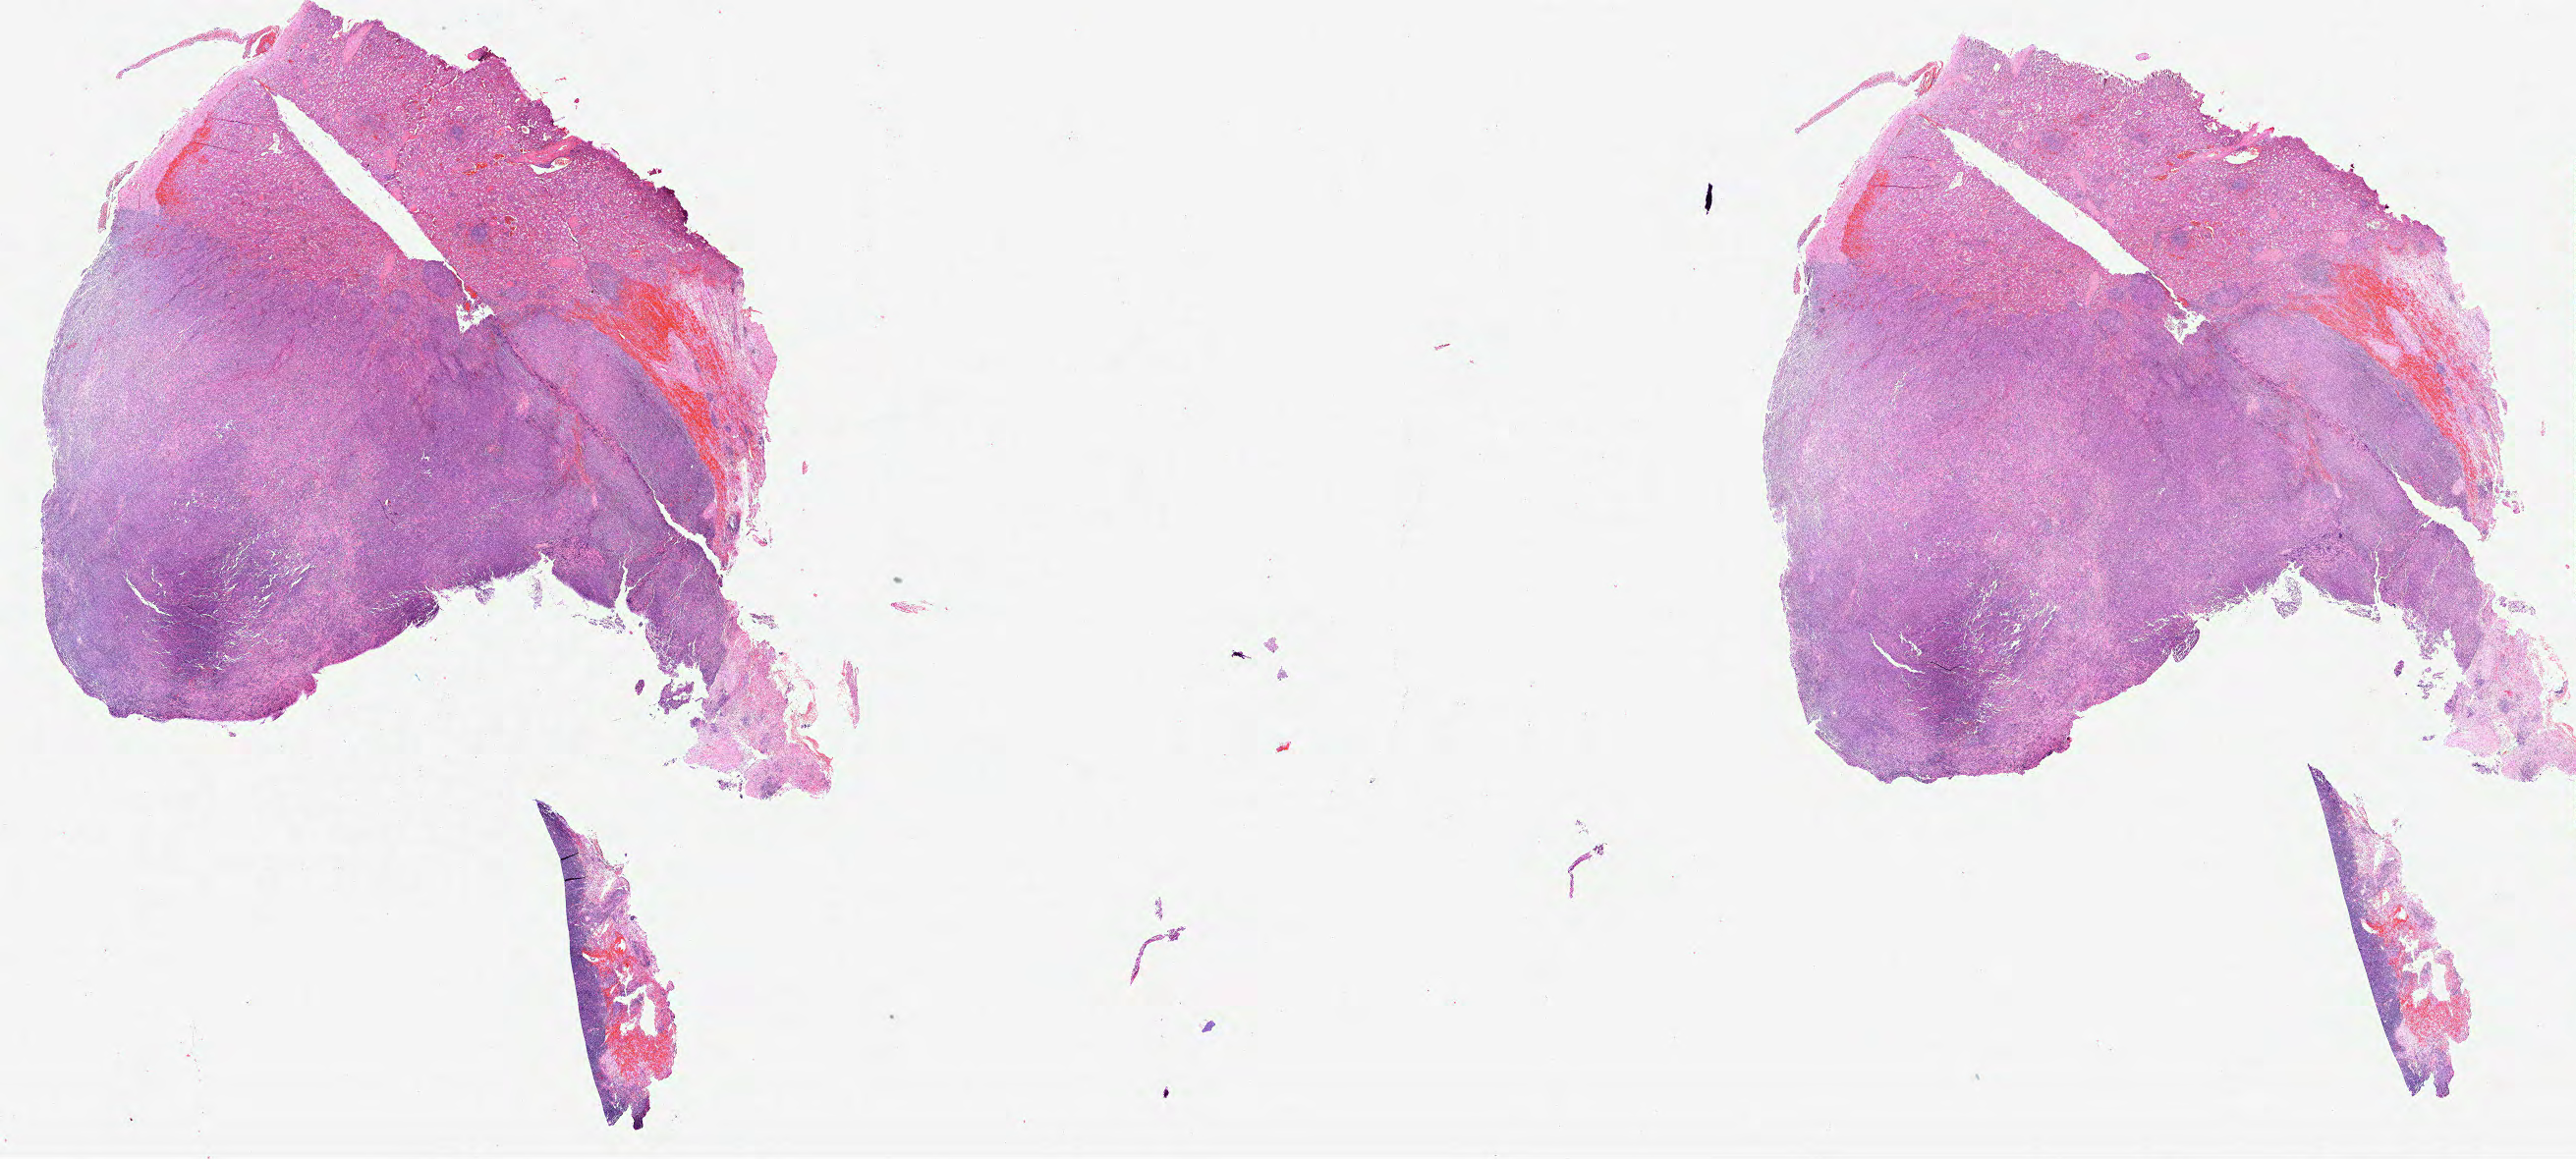
Hematoxylin and eosin (H&E) stained whole-slide image, whole scanned area (about 42.3 x 19.0 mm, from a 40x scan) shown as a low-resolution overview, FFPE section, primary tumour sample from the lymphoid tissue. Male patient; age at initial diagnosis 58 years.
Pathologic diagnosis: Diffuse large B-cell lymphoma, NOS (intra-abdominal lymph nodes).